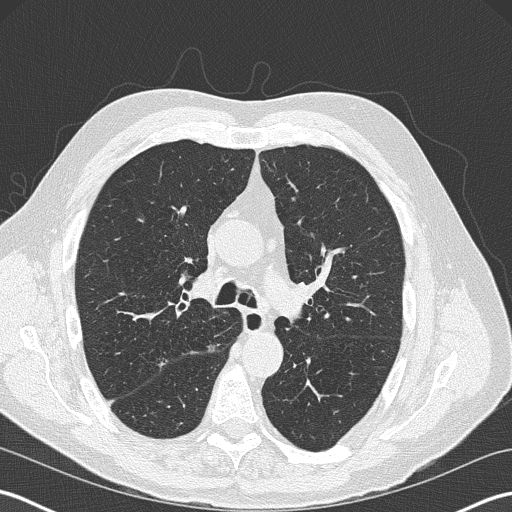
Low-dose screening chest CT, one axial slice. Position 124 of 199 along the scan axis. Reconstruction kernel B50f. 120 kVp. Lung window (W 1500 / L -600 HU). 2 mm slice thickness. 512 × 512 image matrix, field of view 350 × 350 mm.
Outlined on this slice (outlined manually by an expert reader):
- lesion 1 (tumor, upper lobe of right lung): bounding box (x1, y1, x2, y2) in pixels: (154, 351, 173, 374)